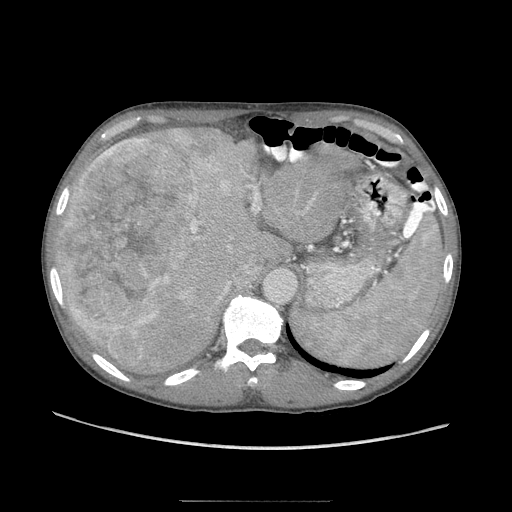
Contrast-enhanced abdominal CT (liver protocol), one axial slice; position 68 of 103 along the scan axis; reconstruction kernel STANDARD; 120 kVp; soft-tissue window (W 400 / L 40 HU); 2.5 mm slice thickness; 512 × 512 image matrix, field of view 380 × 380 mm. From the clinical record (not read from this slice): diagnosis: hepatocellular carcinoma (patient treated with transarterial chemoembolisation; whether this scan precedes or follows treatment is not stated here); TNM stage (as recorded): Stage-IIIA; Child-Pugh class: A; tumour nodularity: multinodular; tumour size: 16 cm.
Annotated regions visible in this slice (semi-automatically segmented with operator editing):
- liver parenchyma outside the tumour (the mass and vessels are separate outlines, so this box may not span the whole liver): box from (x=56, y=128) to (x=326, y=370) px
- mass: (x=60, y=138)–(x=199, y=370)
- liver vessels: (x=130, y=216)–(x=200, y=333)